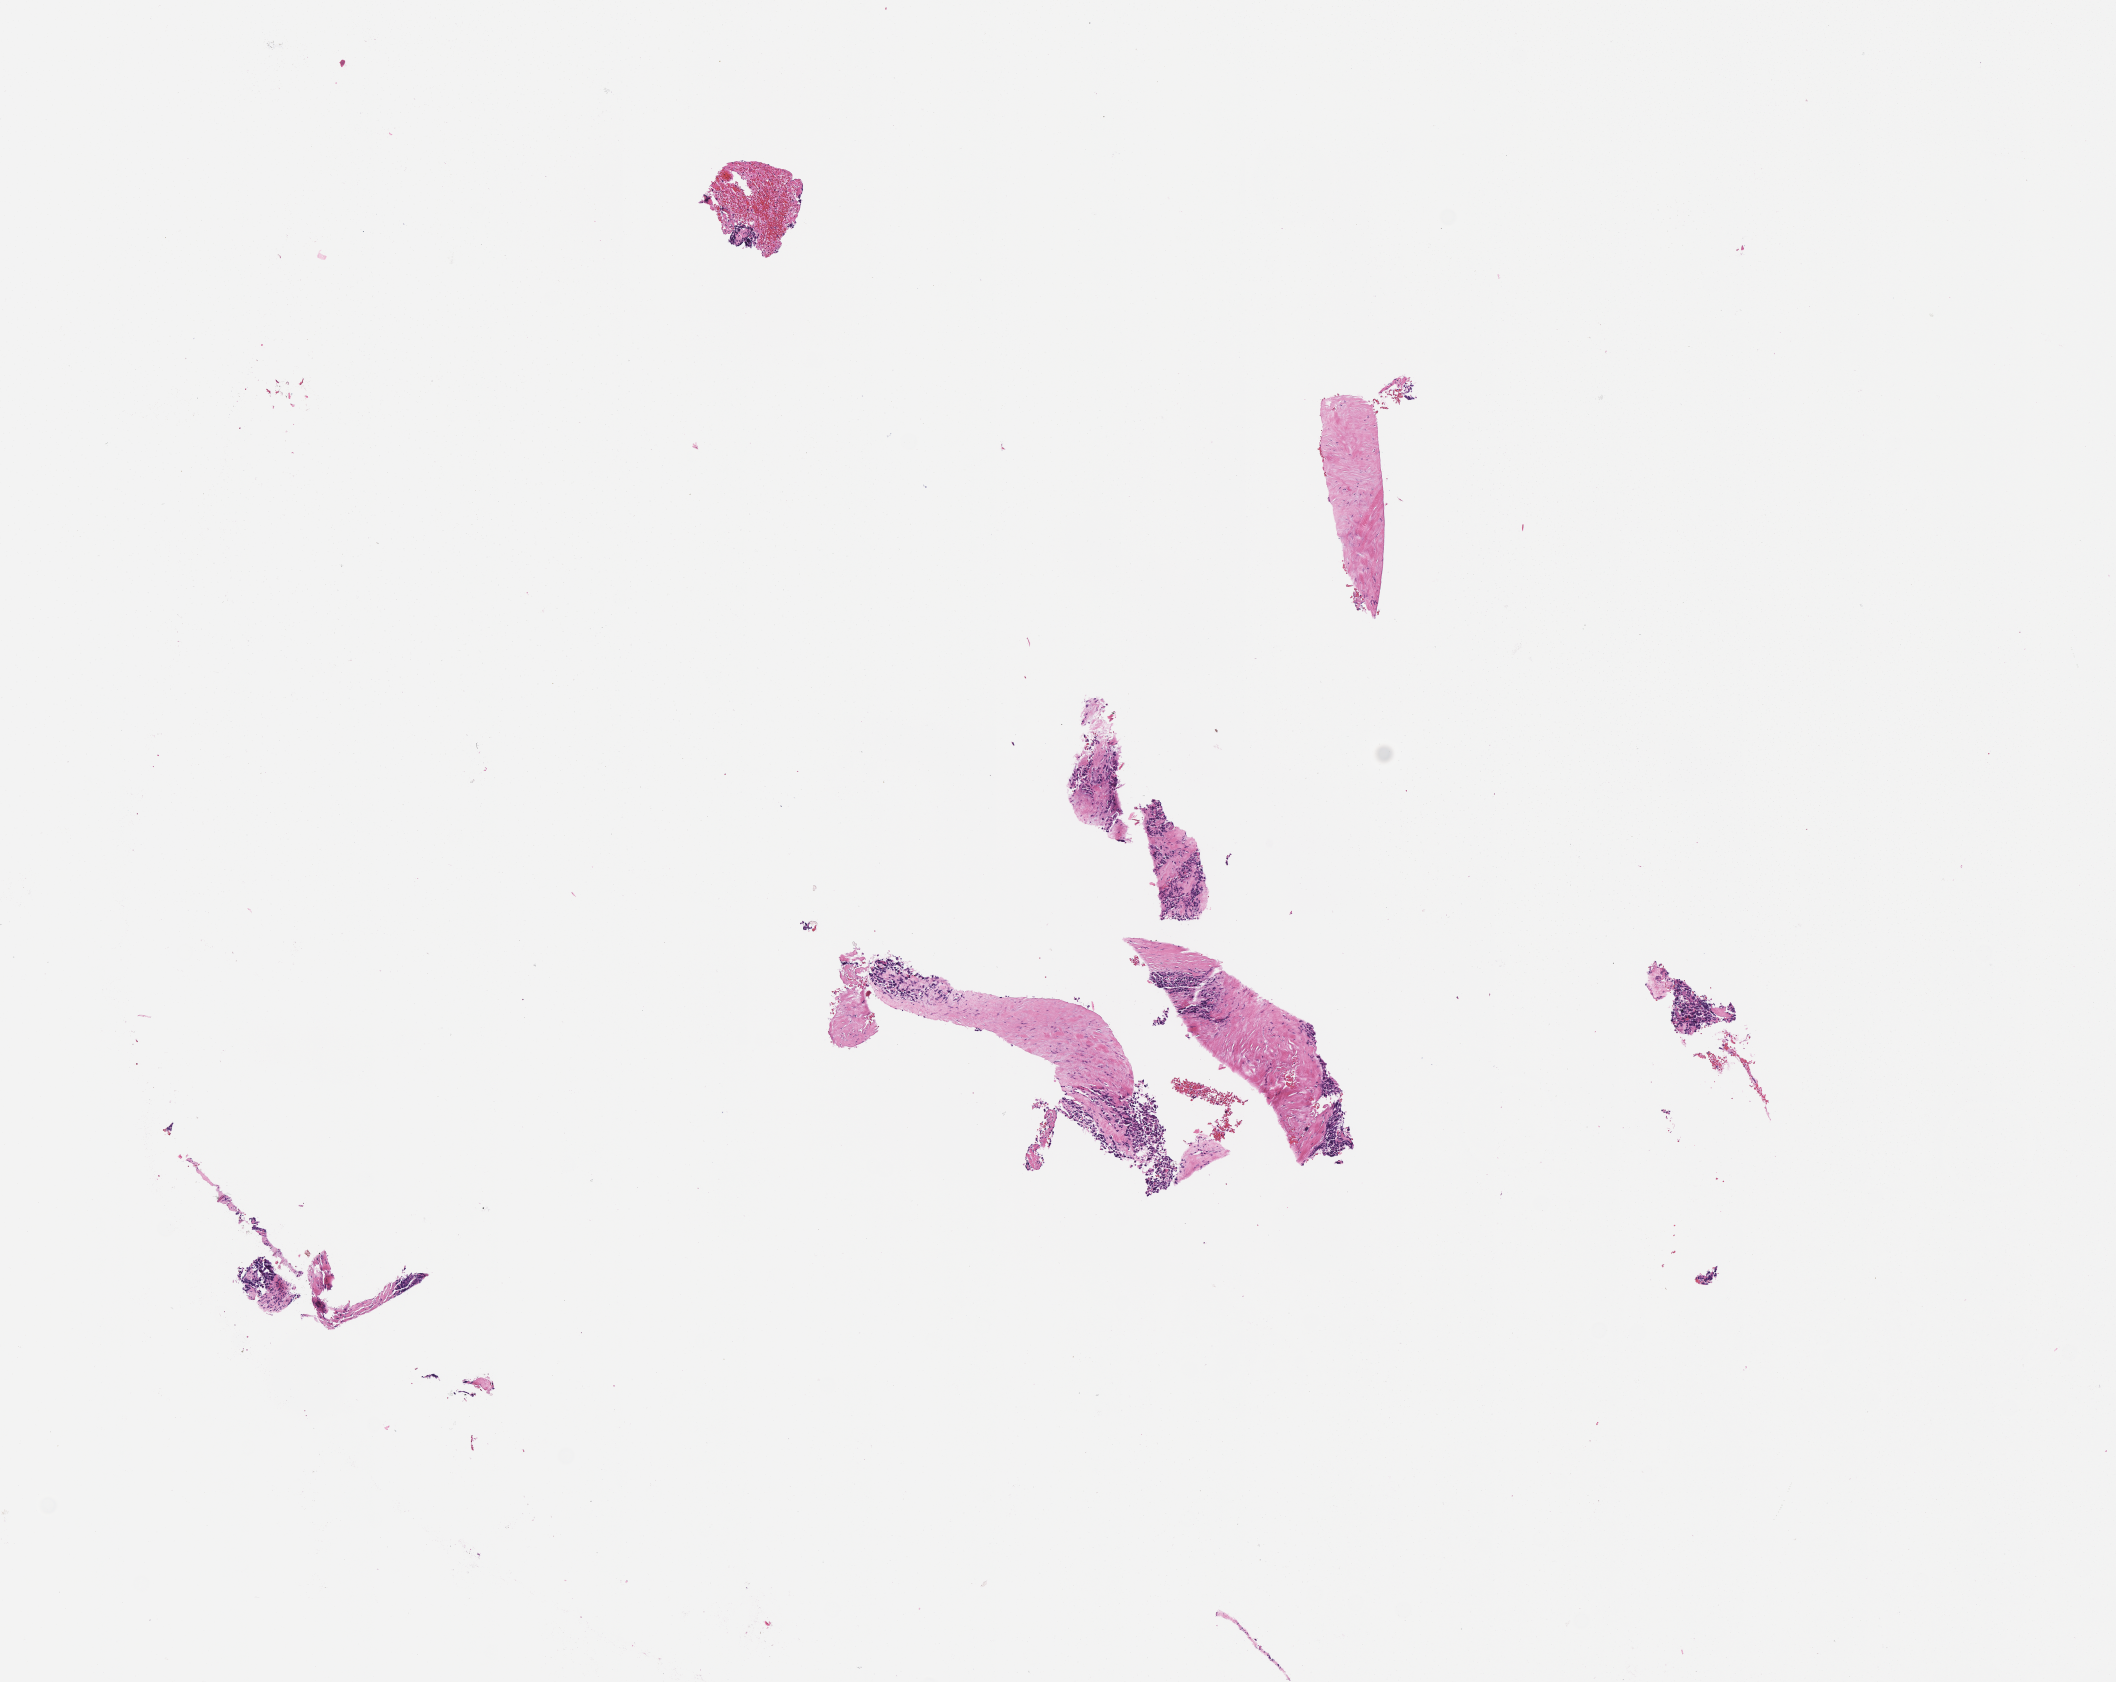
Haematoxylin and eosin whole-slide image of tumor tissue — low-resolution overview of the scanned area, about 8.6 x 6.8 mm; formalin-fixed, paraffin-embedded (FFPE) tissue; sample anatomic site: soft tissue, arm-right. Patient: male, age 16.5 years at diagnosis.
* diagnosis: rhabdomyosarcoma; histological classification: rhabdomyosarcoma nos
* stage (as recorded): 4
* metastatic status at presentation (as recorded): metastatic (confirmed)